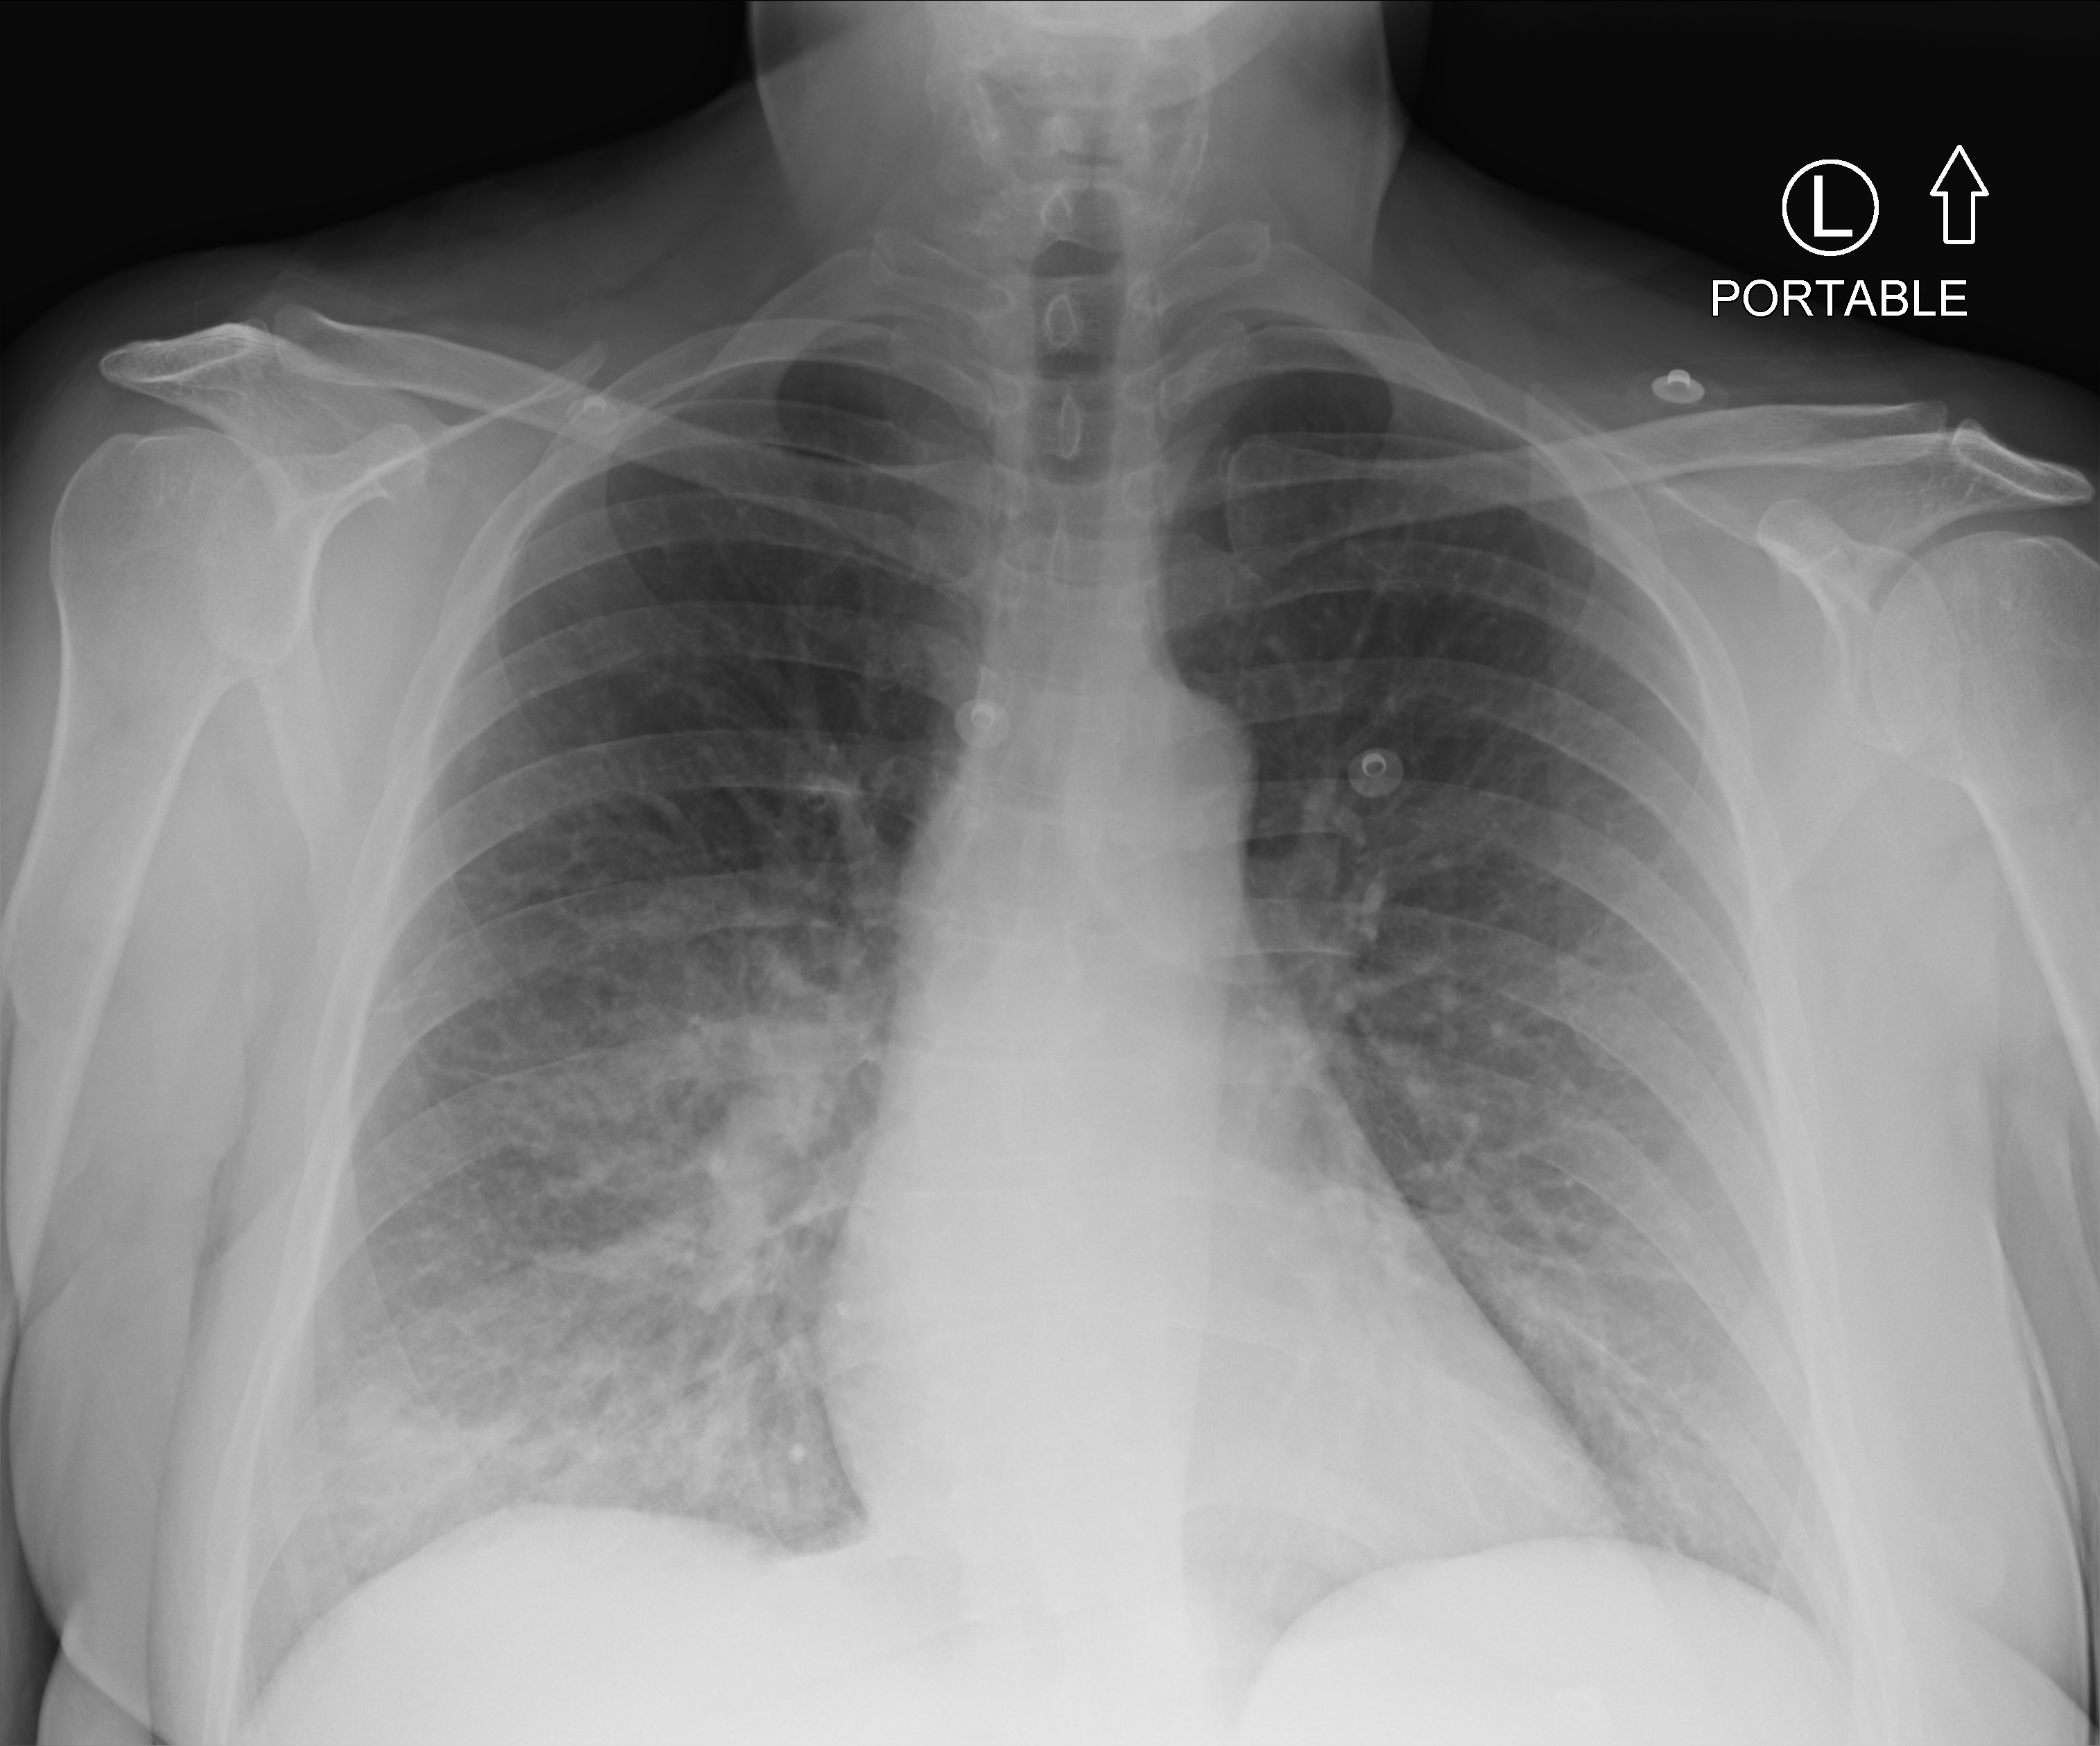
Portable chest radiograph, anteroposterior (AP) projection. Female patient hospitalised with COVID-19, age 18–59 years.
From the hospital-stay record, not from the radiograph (when in the stay this image was taken is not recorded): COPD (admission record): no; admitted to intensive care during this hospital stay: yes; other chronic lung disease (admission record): no.